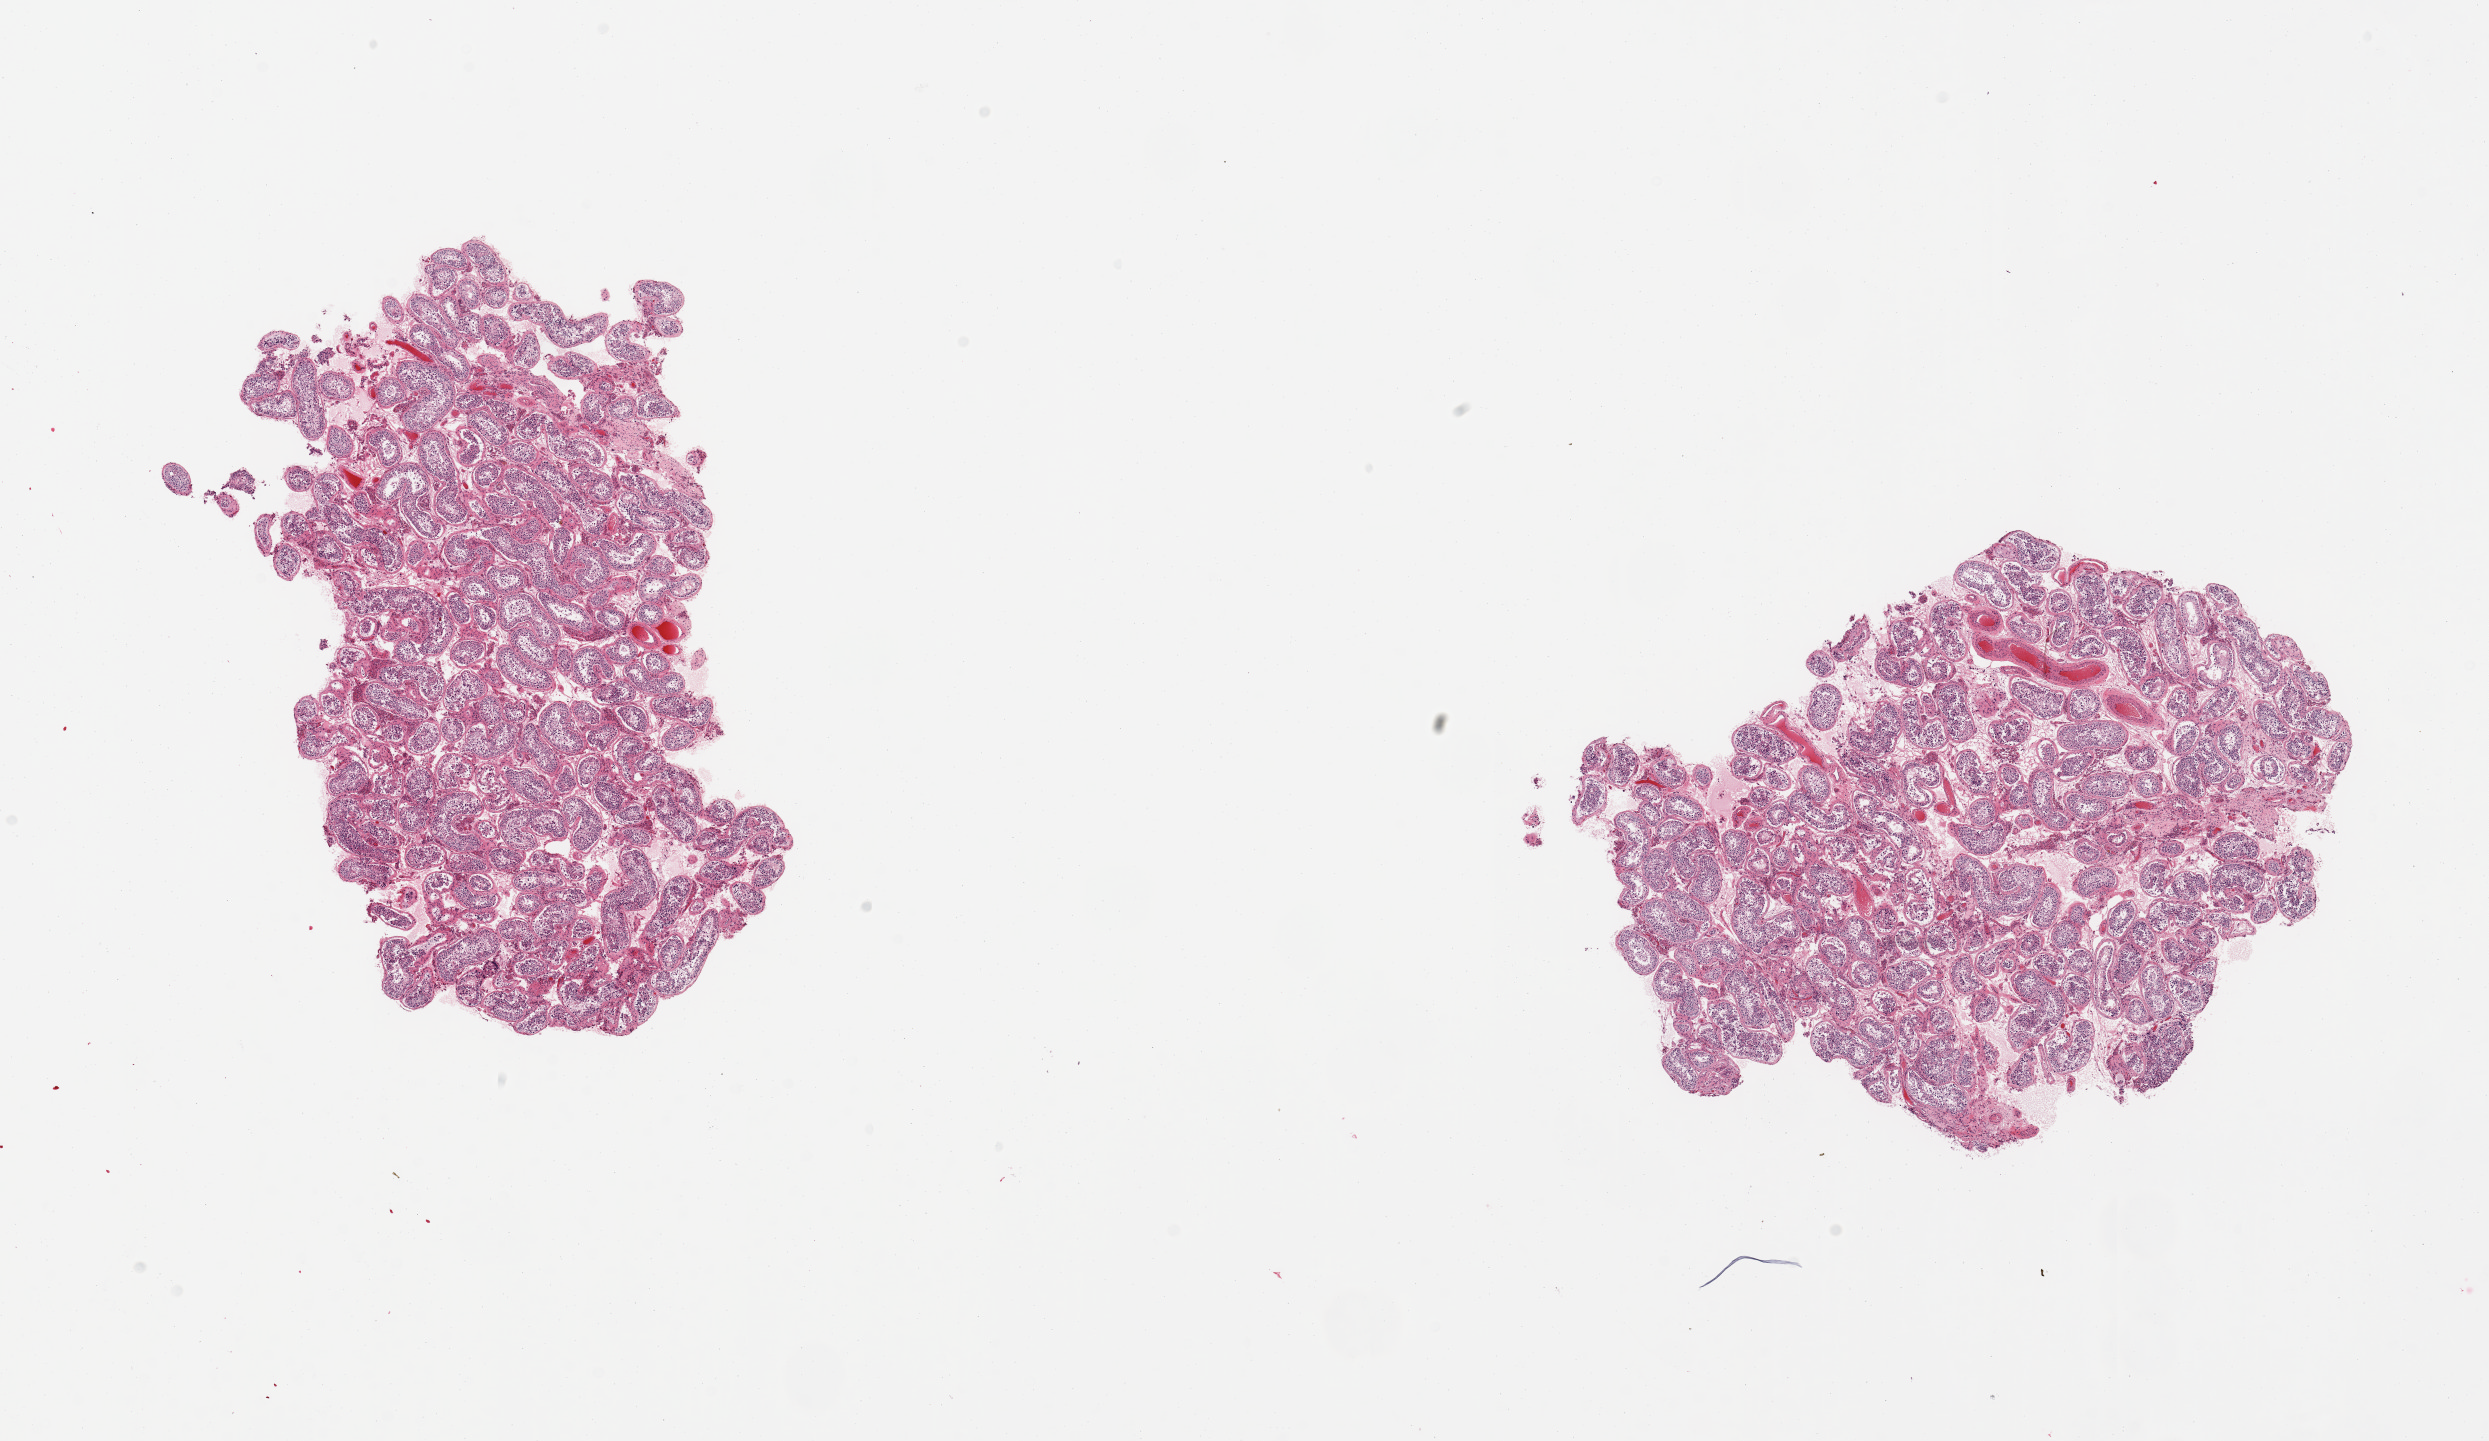
Digitized hematoxylin and eosin (H&E)-stained section, whole scanned area (about 19.7 x 11.4 mm) shown as a low-resolution overview. PAXgene-fixed, paraffin-embedded tissue. Target tissue: testis. Tissue donor sample.
• reviewer comment on this tissue sample: 2 pieces, spermatogenesis is present